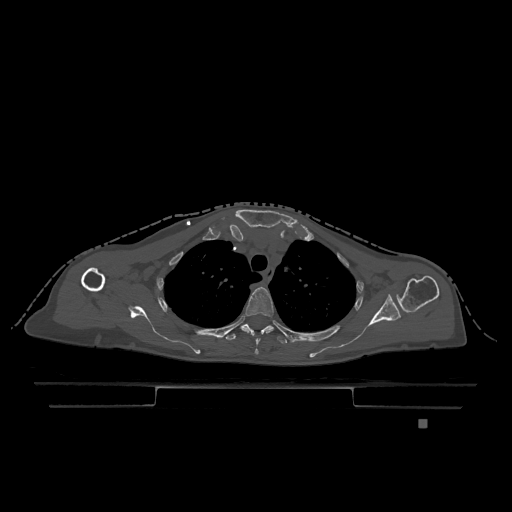
CT including the spine, one axial slice; slice 909 of 1317 in the series (ordered by position); bone window (W 1800 / L 400 HU); 0.5 mm slice thickness; 512 × 512 image matrix, field of view 500 × 500 mm. Patient: female, 74 years. Case-level facts recorded for this patient, not image findings: primary cancer: lung.
Annotated regions visible in this slice (semi-automatically segmented with operator editing):
- T3 vertebra: bounding box [x1, y1, x2, y2] px = [240, 287, 274, 354]
- T4 vertebra: [226, 324, 307, 344]